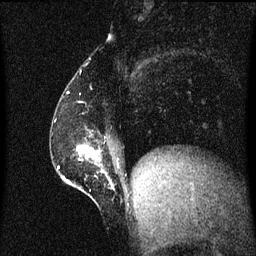
Breast MRI (dynamic contrast-enhanced), one sagittal slice; position 18 of 60 along the scan axis; dynamic contrast-enhanced series, image 2 of 3 at this slice position (ordered by acquisition); 1.5 T; TE 4.2 ms, TR 8.4 ms; 2 mm slice thickness; 256 × 256 image matrix. Patient: female, 52 years. From the clinical record (not read from this slice): setting: breast cancer imaged before/during neoadjuvant chemotherapy; receptor status: HER2-positive.
Annotated regions visible in this slice (semi-automatically segmented with operator editing):
- analysis volume of interest (the breast-tissue region the enhancement analysis was run in; not a lesion): bounding box [x1, y1, x2, y2] px = [62, 134, 115, 203]
- tumour enhancement mask (voxels above the 70 % enhancement threshold inside the analysis volume of interest): [77, 146, 105, 173]